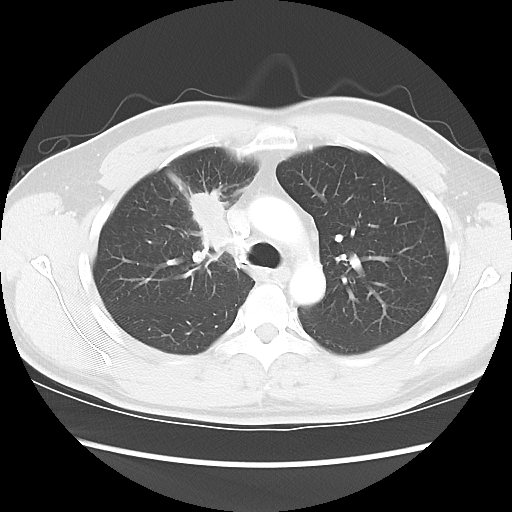
Chest CT, one axial slice. Slice 63 of 80 in the series (ordered by position). Reconstruction kernel LUNG. Lung window (W 1500 / L -600 HU). 512 × 512 image matrix, field of view 360 × 360 mm. Male patient, age 35 years. Case-level facts recorded for this patient, not image findings: clinical TNM (as recorded): T1c N1 M1b.
Outlined on this slice (rectangle marked by the reading radiologist):
- lung tumour (recorded histology: adenocarcinoma): bounding box (x1, y1, x2, y2) in pixels: (183, 186, 232, 251)